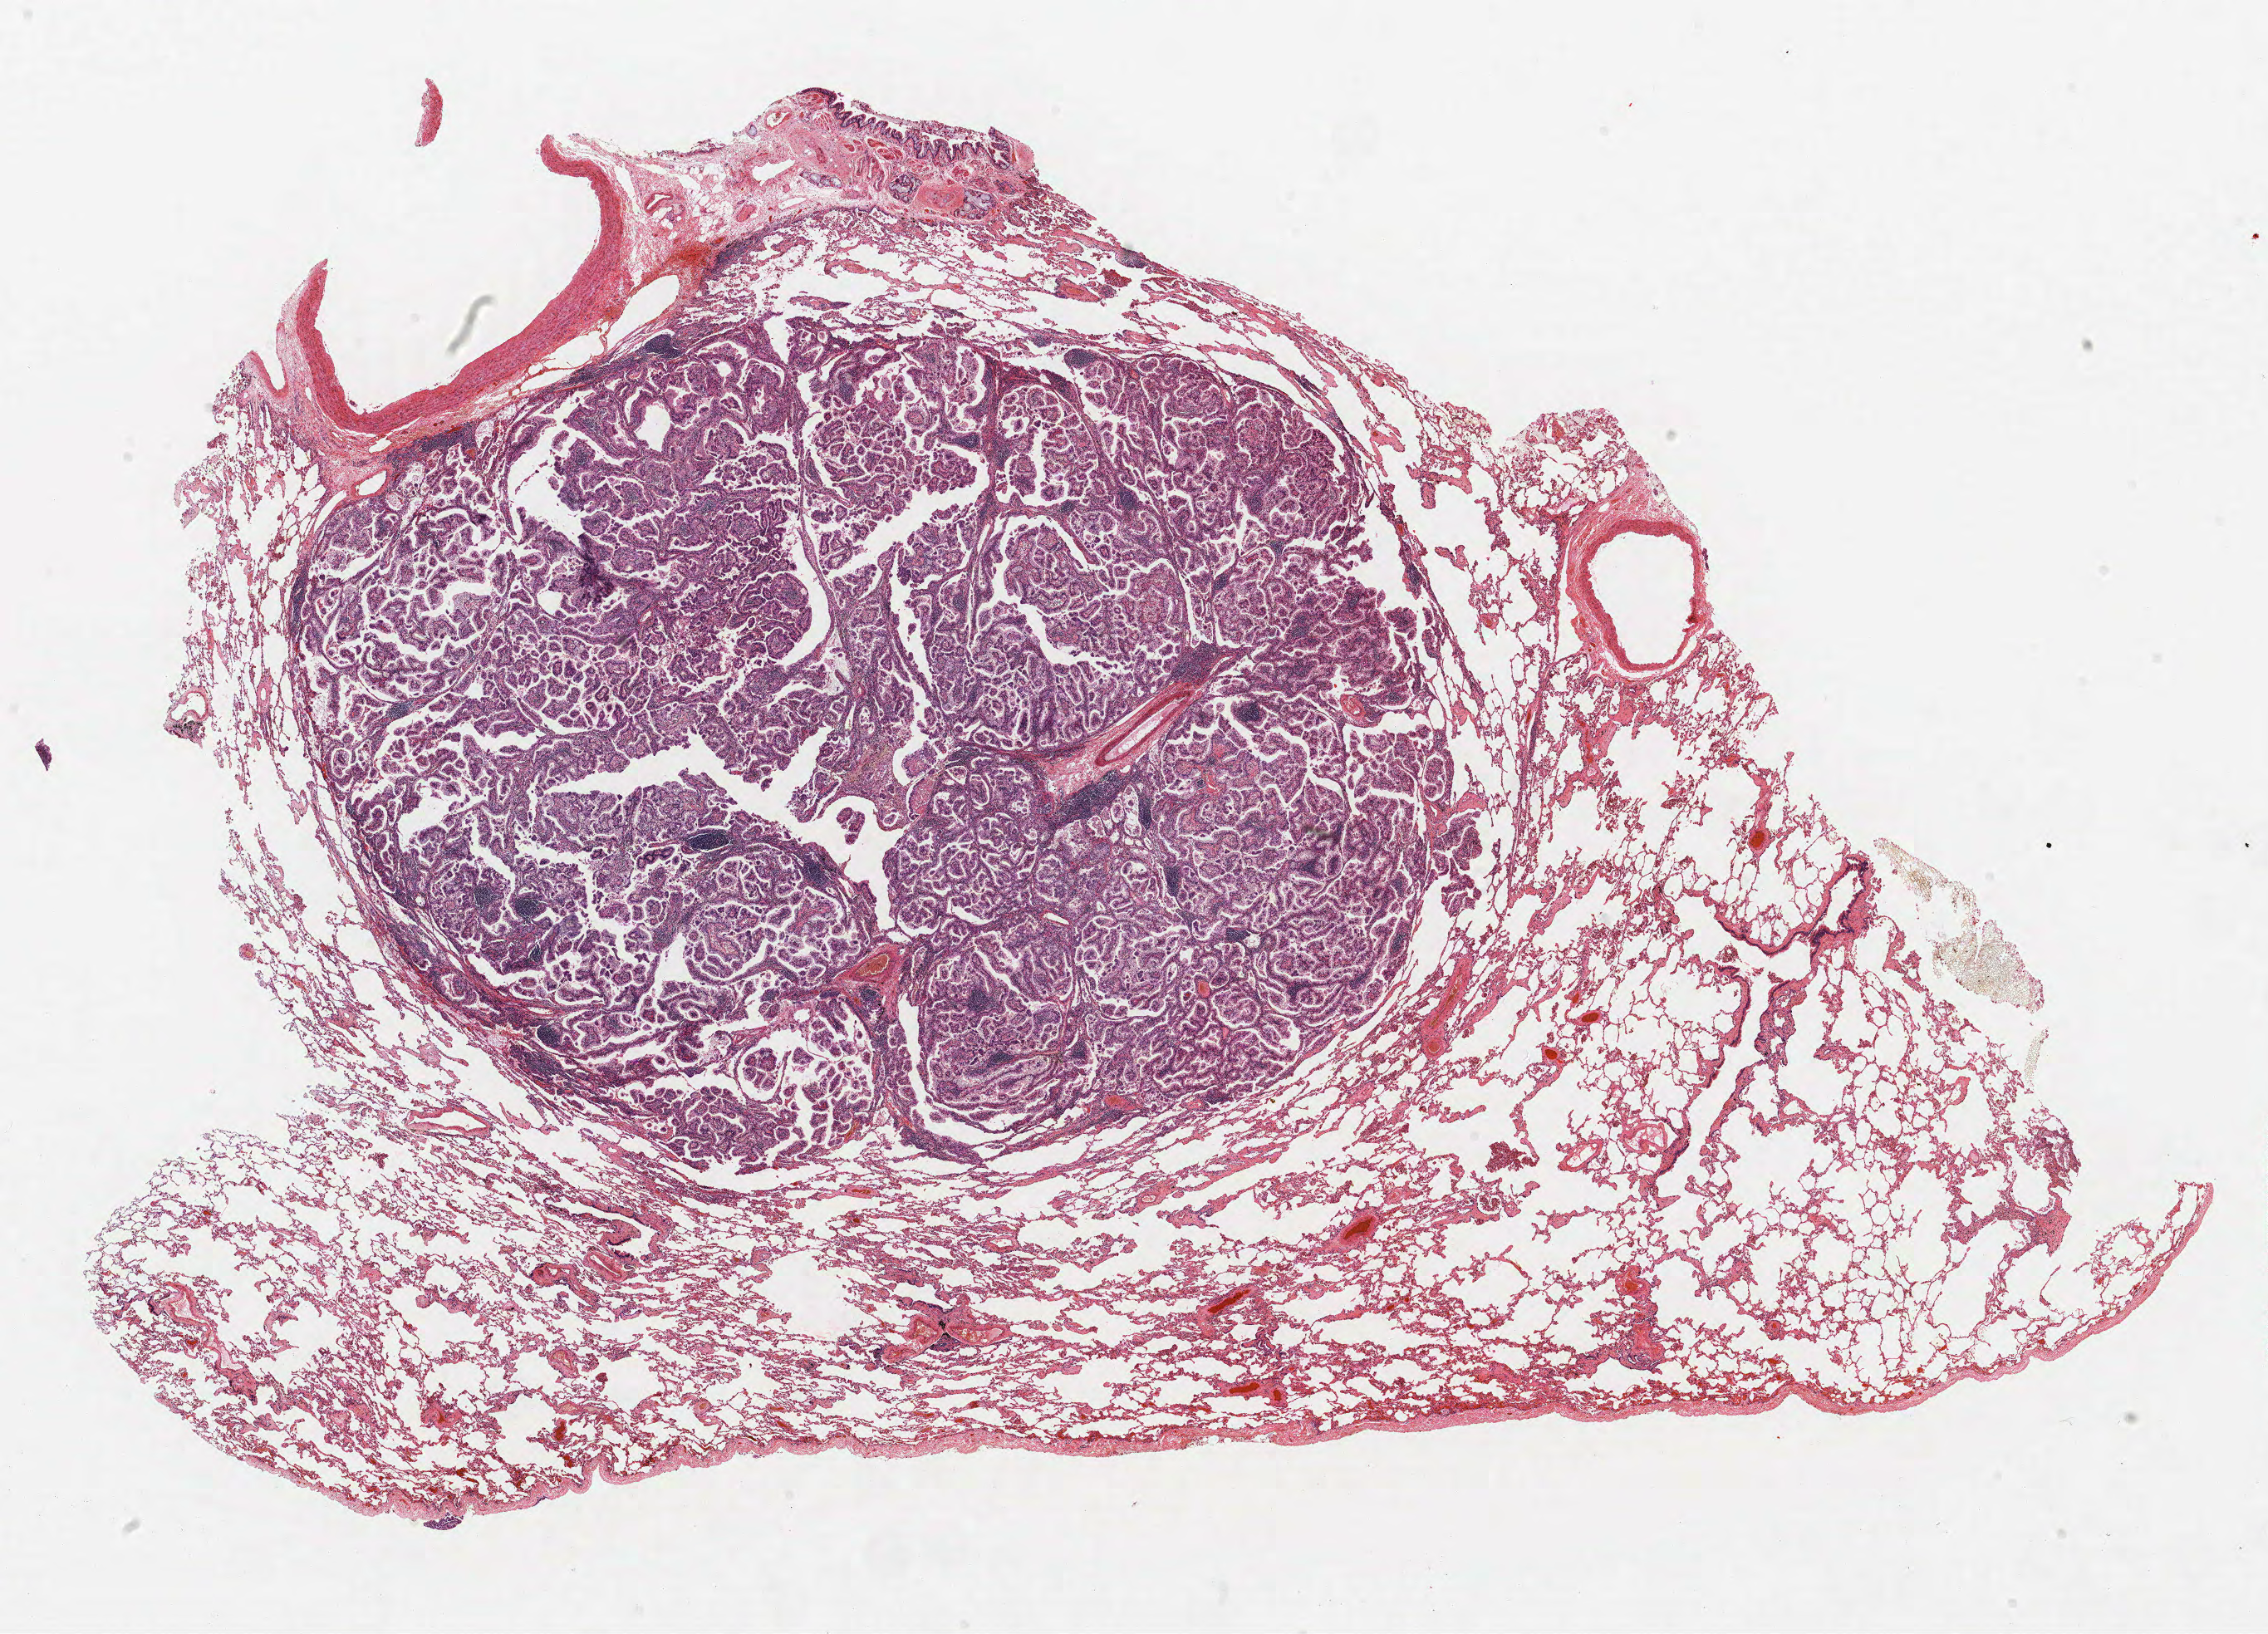
Hematoxylin and eosin (H&E) stained whole-slide image, whole scanned area (about 21.8 x 15.7 mm) shown as a low-resolution overview, formalin-fixed paraffin-embedded (FFPE) section, lung. Male patient, aged 61 at enrolment. Current smoker at enrolment. Grade: well differentiated (G1).
Stage (AJCC 6th edition): IA. Tumour size (pathology): 15 mm. Participant's lung-cancer diagnosis: Bronchiolo-alveolar adenocarcinoma, NOS (ICD-O-3 8250/3). Primary tumour location (clinical record): right middle lobe.